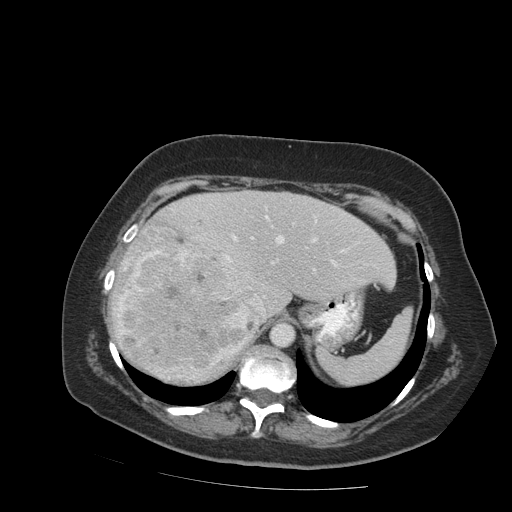
Contrast-enhanced abdominal CT (liver protocol), one axial slice. Reconstruction kernel STANDARD. 140 kVp. Soft-tissue window (W 400 / L 40 HU). 2.5 mm slice thickness. 512 × 512 image matrix. Case-level facts recorded for this patient, not image findings: diagnosis: hepatocellular carcinoma (patient treated with transarterial chemoembolisation; whether this scan precedes or follows treatment is not stated here); TNM stage (as recorded): Stage-IVB; Child-Pugh class: A; tumour differentiation: moderately differentiated; tumour nodularity: uninodular.
Annotated regions visible in this slice (semi-automatically segmented with operator editing):
- abdominal aorta: bounding box (x1, y1, x2, y2) in pixels: (270, 322, 294, 347)
- liver parenchyma outside the tumour (the mass and vessels are separate outlines, so this box may not span the whole liver): (112, 190, 396, 384)
- mass: (113, 224, 258, 384)
- liver vessels: (225, 208, 345, 310)